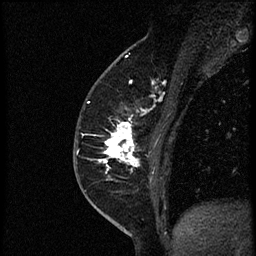
Breast MRI (dynamic contrast-enhanced), one sagittal slice. Position 23 of 56 along the scan axis. Dynamic contrast-enhanced study with each time point stored as its own series, time point 2 of 4 at this slice position (early post-contrast, ordered by acquisition time). 1.5 T. TE 4.2 ms, TR 18.9 ms. 256 × 256 image matrix. Female patient. Case-level facts recorded for this patient, not image findings: setting: breast cancer imaged before/during neoadjuvant chemotherapy; receptor status: HER2-positive.
Outlined on this slice (semi-automatically segmented with operator editing):
- analysis volume of interest (the breast-tissue region the enhancement analysis was run in; not a lesion): bounding box <97,86,174,189> (left, top, right, bottom; pixels)
- tumour enhancement mask (voxels above the 100 % enhancement threshold inside the analysis volume of interest): <100,97,163,174>